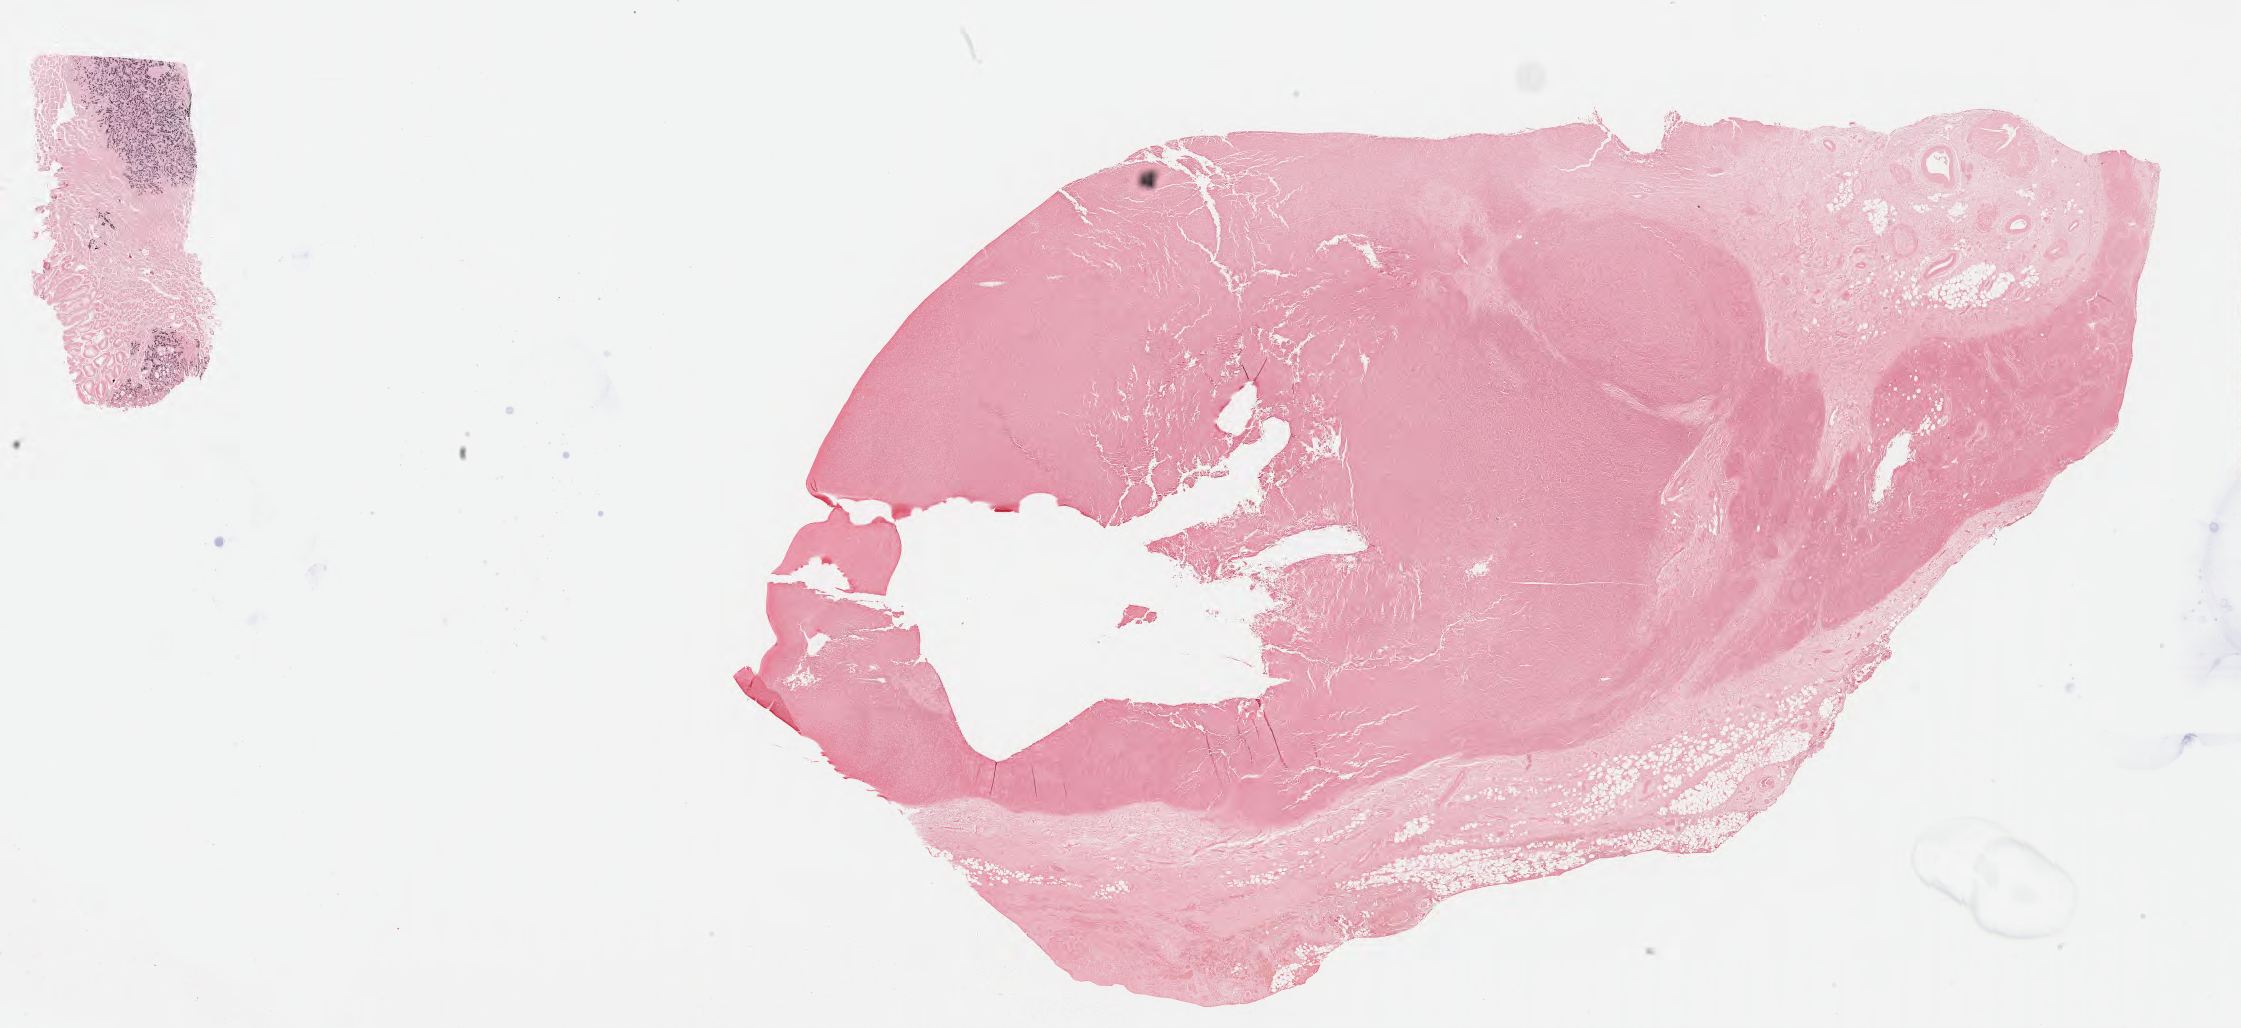
Whole-slide image, Epstein–Barr virus-encoded RNA (EBER) in-situ hybridisation — whole scanned area (about 36.2 x 16.6 mm) shown as a low-resolution overview; tumor tissue; site: lymph node. Patient male; aged 60.
Histologic diagnosis: Diffuse large B-cell lymphoma, NOS.